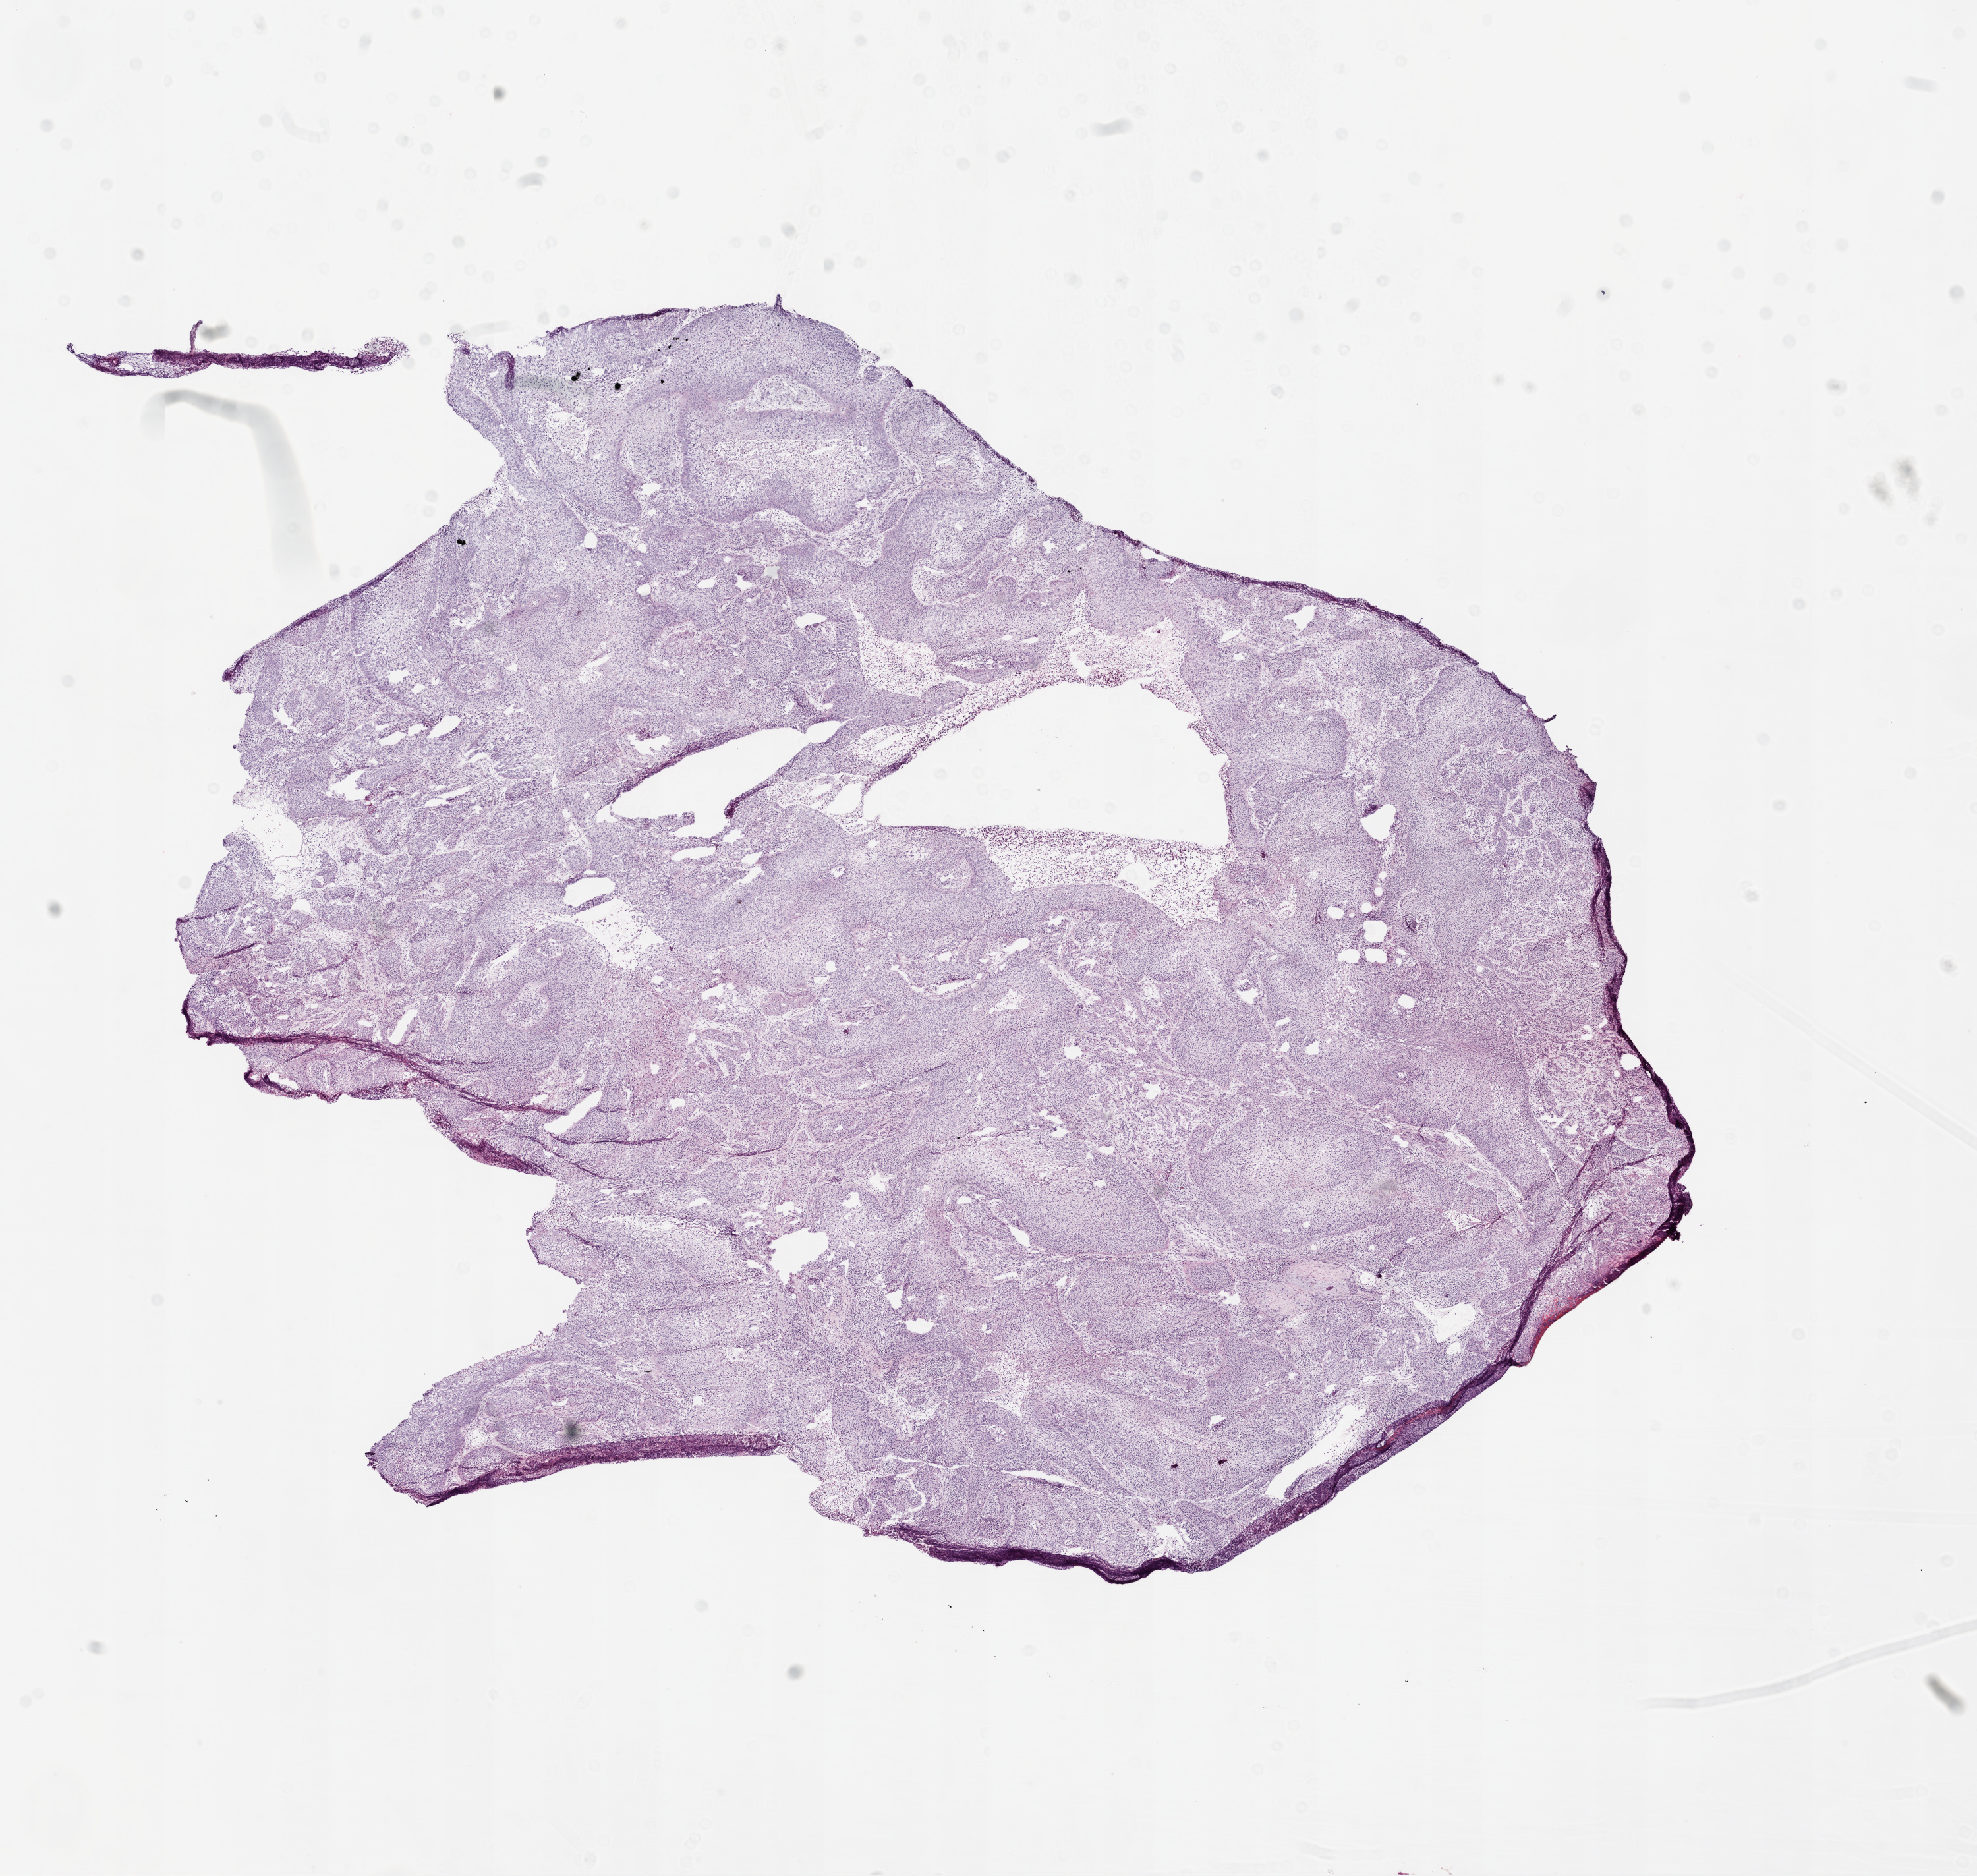
H&E-stained whole-slide image — a low-resolution overview of the entire scanned area, about 12.0 x 11.4 mm, frozen section, primary tumour sample from the lung. Male, age 73 years at initial diagnosis. Slide review estimates, as recorded: tumour cells 85%, tumour nuclei 85%, normal cells 0%, stromal cells 3%, necrosis 12%.
Histologic diagnosis: Squamous cell carcinoma, NOS. AJCC pathologic stage: IB.